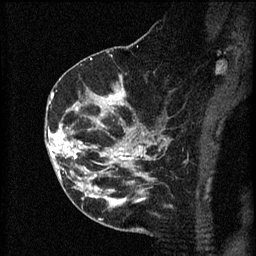
Breast MRI (dynamic contrast-enhanced), one sagittal slice; slice 33 of 60 in the series (ordered by position); 3 images stored at this slice position (order not interpretable as contrast timing); 1.5 T; TE 4.2 ms, TR 8.2 ms; 256 × 256 image matrix. Patient: female, 49 years.
Outlined on this slice (semi-automatic segmentation, software-assisted and operator-edited):
- analysis volume of interest (the breast-tissue region the enhancement analysis was run in; not a lesion): bounding box [x1, y1, x2, y2] px = [45, 126, 105, 177]
- tumour enhancement mask (voxels above the 70 % enhancement threshold inside the analysis volume of interest): [48, 126, 97, 177]